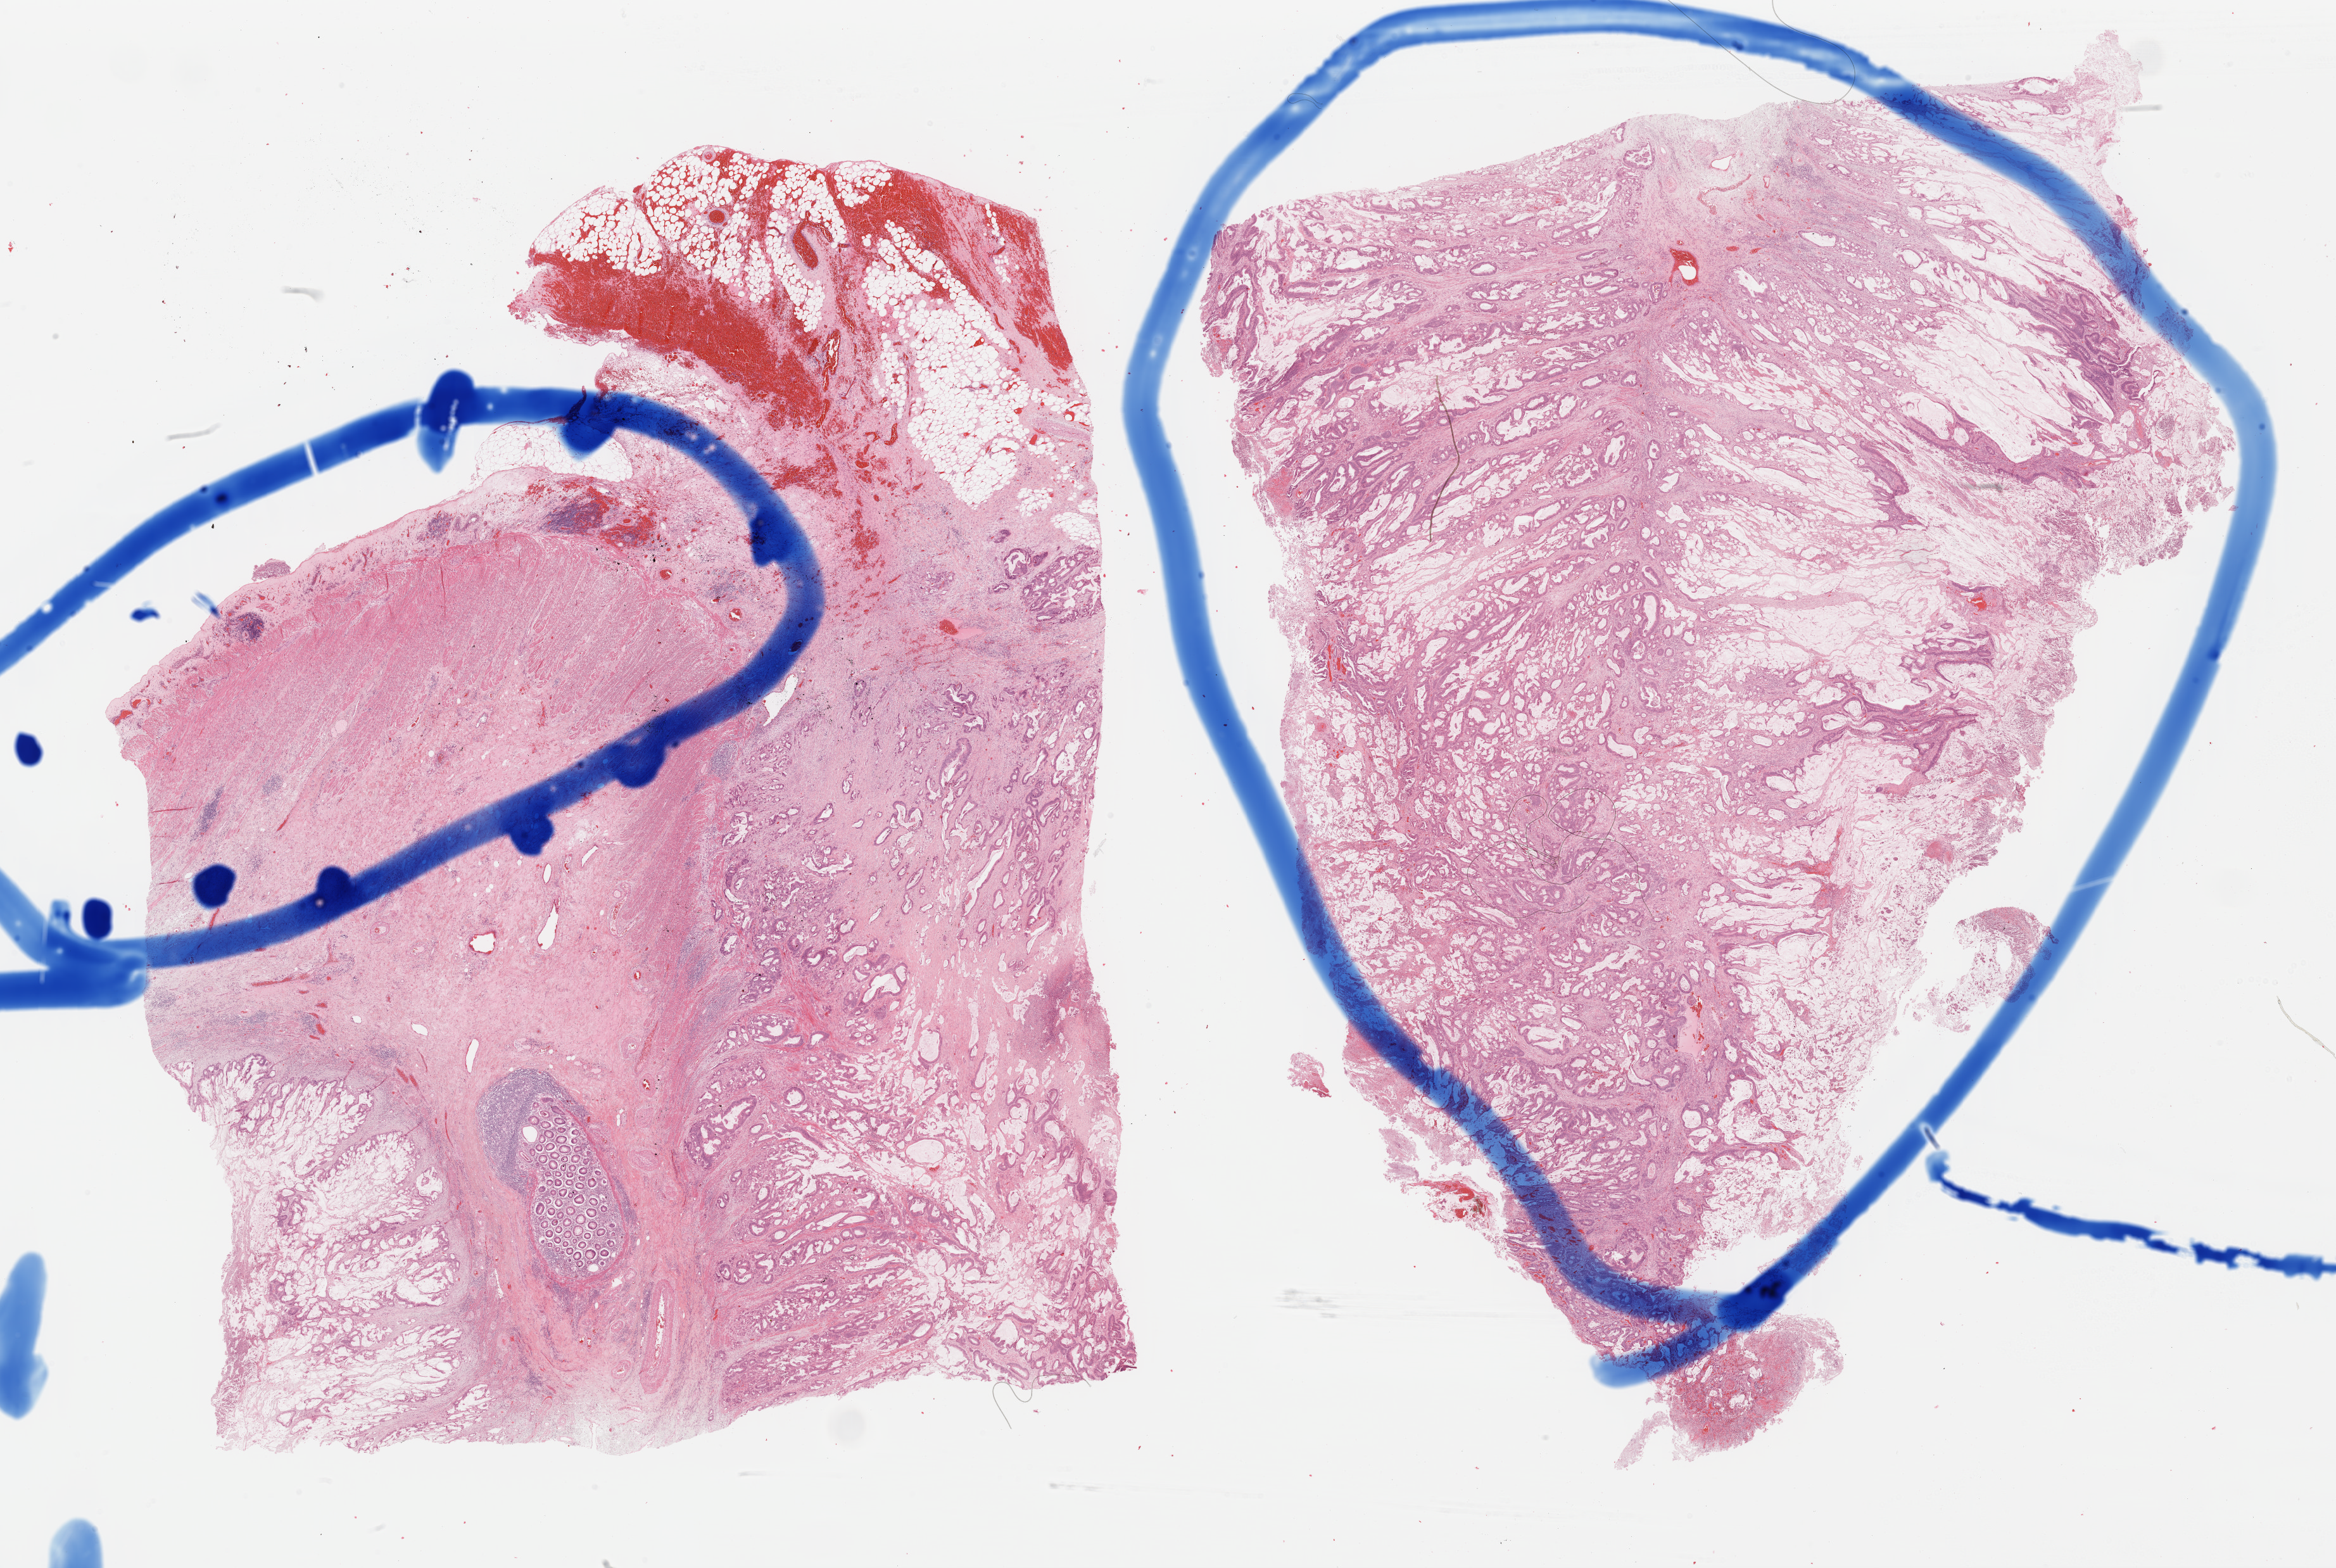
H&E whole-slide image, whole scanned area (about 29.1 x 19.6 mm, from a 40x scan) shown as a low-resolution overview, formalin-fixed paraffin-embedded (FFPE) diagnostic section, primary tumour sample from the colon. Male patient; age at initial diagnosis 68 years.
- pathologic diagnosis: Mucinous adenocarcinoma (cecum)
- AJCC pathologic stage: IIIC (6th edition)